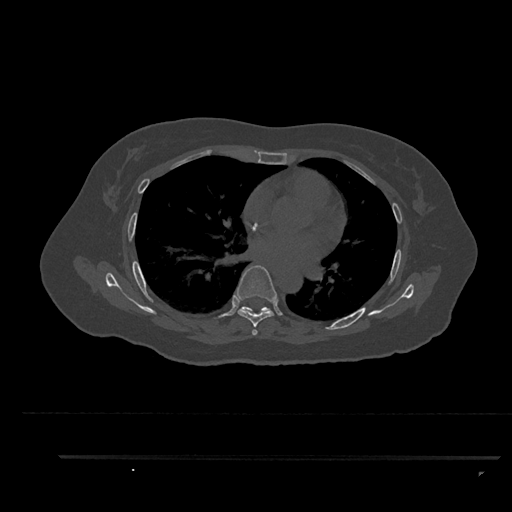
CT including the spine, one axial slice; slice 547 of 797 in the series (ordered by position); bone window (W 1800 / L 400 HU); 0.5 mm slice thickness; 512 × 512 image matrix. Patient: female, 44 years. Case-level facts recorded for this patient, not image findings: primary cancer: renal; vertebrae with lytic lesions (as recorded): L1.
Annotated regions visible in this slice (semi-automatically segmented with operator editing):
- T6 vertebra: bounding box <235,265,277,335> (left, top, right, bottom; pixels)
- T7 vertebra: <242,306,270,314>